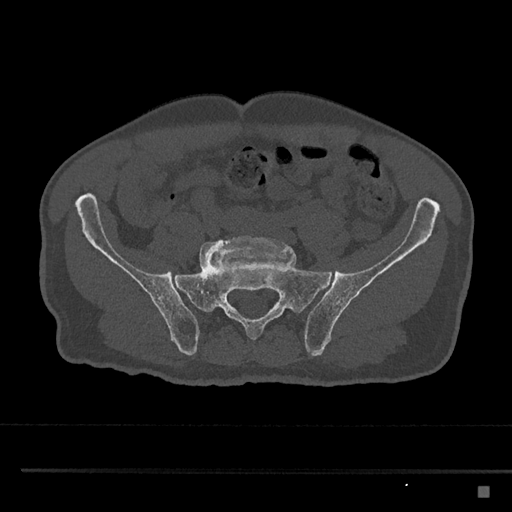
CT including the spine, one axial slice. Slice 540 of 797 in the series (ordered by position). Reconstruction kernel Br40s/3. 120 kVp. Bone window (W 1800 / L 400 HU). 512 × 512 image matrix. Patient: male, 59 years. From the clinical record (not read from this slice): primary cancer: prostate.
Annotated regions visible in this slice (semi-automatically segmented with operator editing):
- L5 vertebra: bounding box (x1, y1, x2, y2) in pixels: (199, 235, 292, 271)